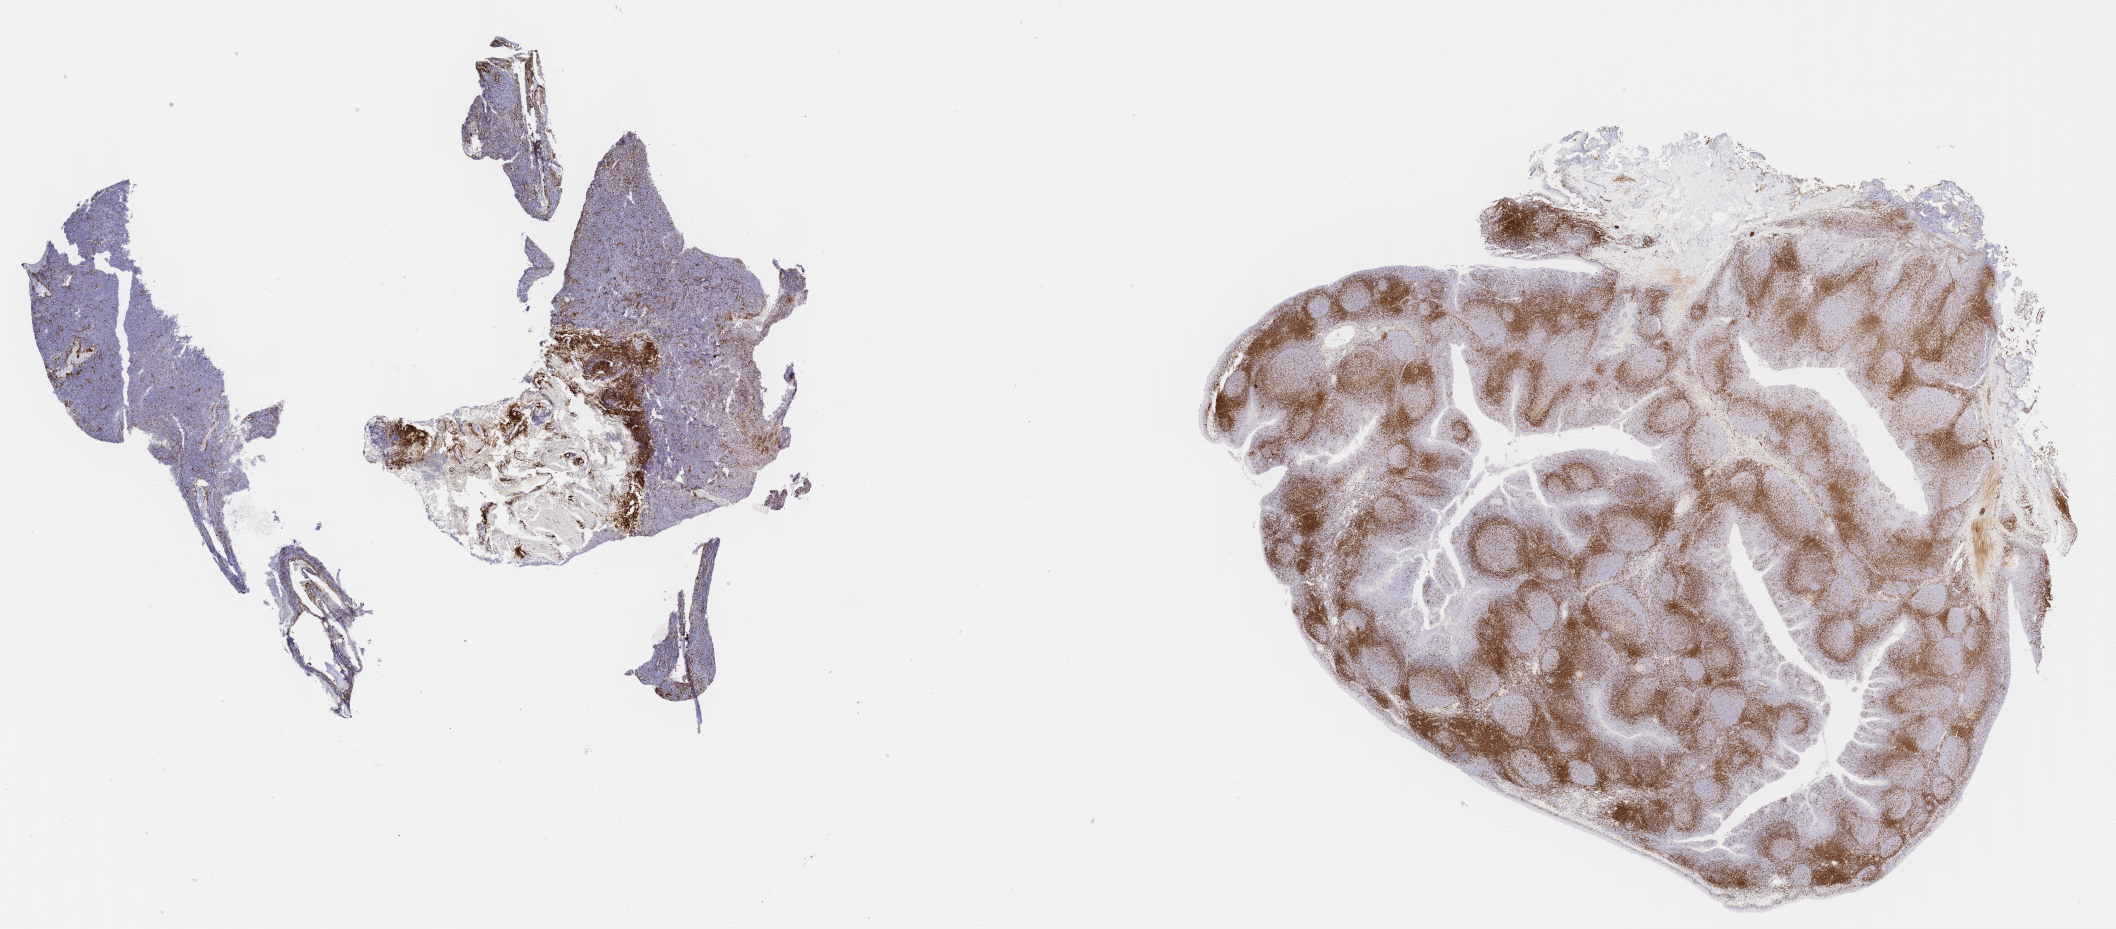
Immunohistochemistry (IHC) whole-slide image stained for CD3 — shown as a low-resolution overview of the whole scanned area (about 34.2 x 15.0 mm); tumor tissue; anatomic site: cranium. Male, age 8 years at initial diagnosis.
Histologic diagnosis: Burkitt lymphoma, NOS.